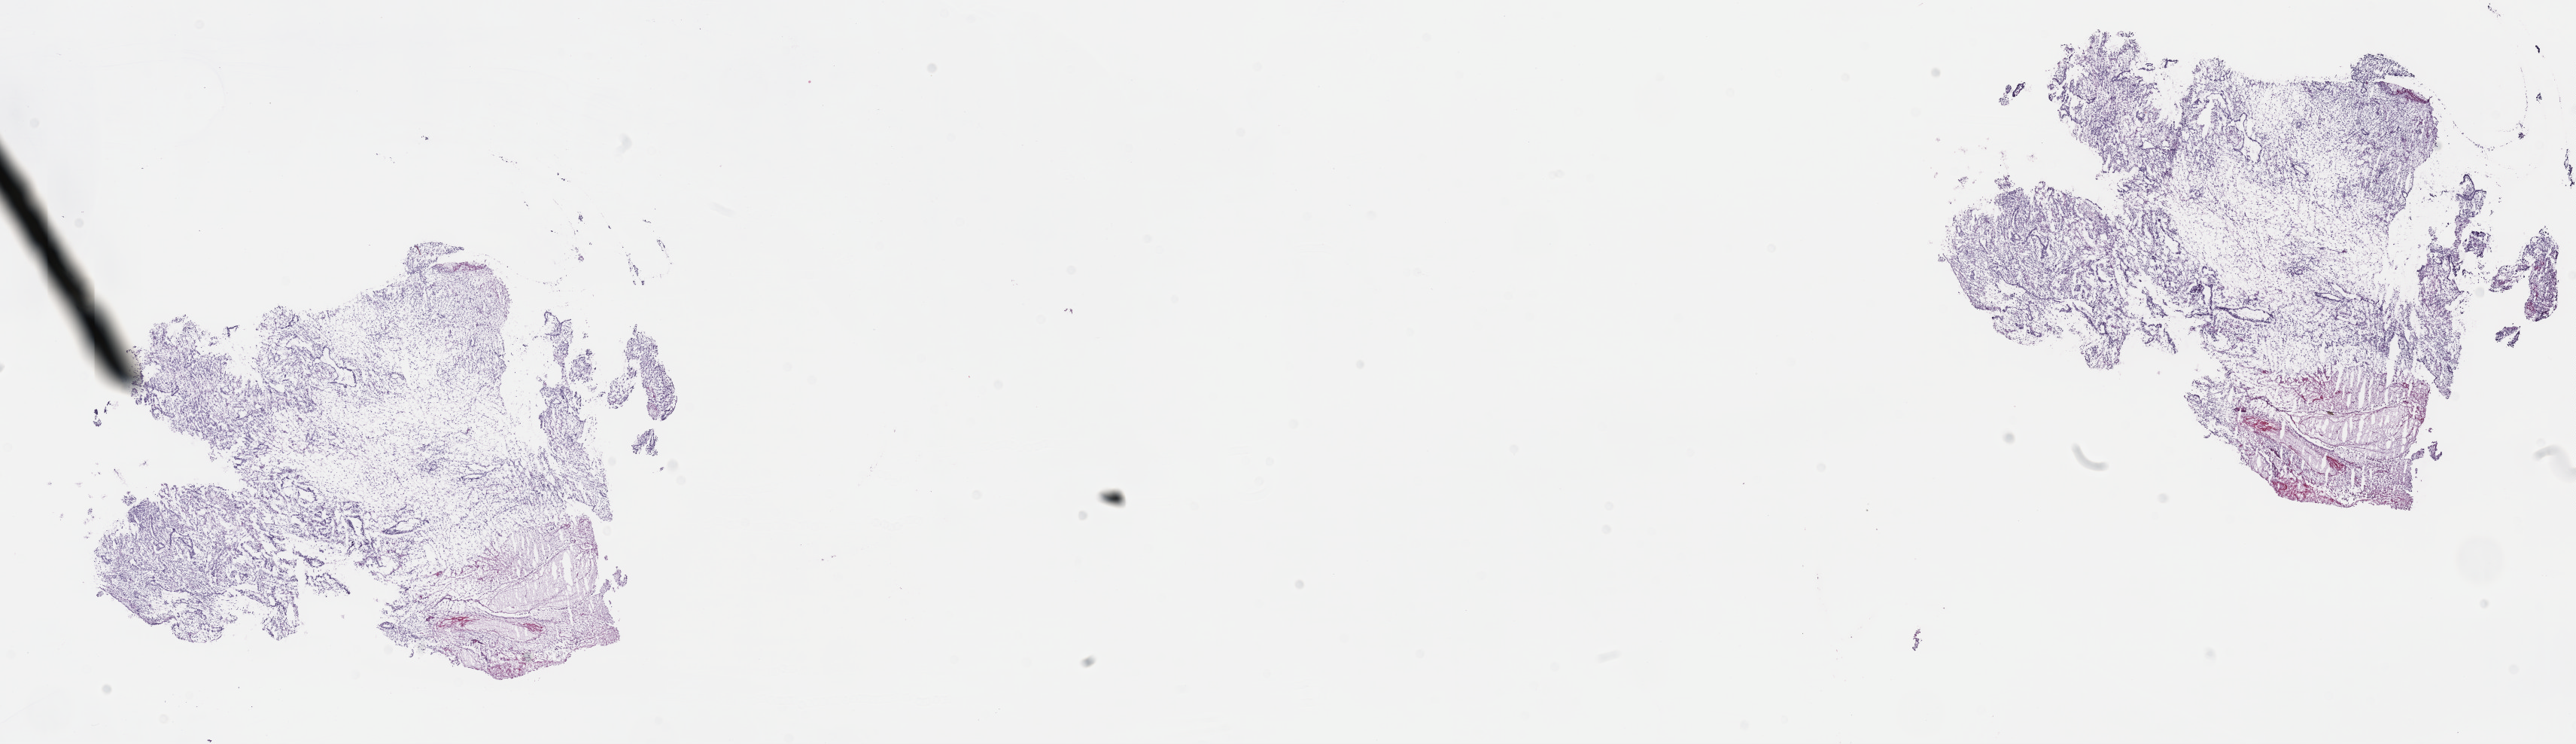
Digitized H&E tissue section (whole slide) — low-resolution overview of the scanned area, about 27.7 x 8.0 mm (slide scanned at 40x), frozen section from the top of the tissue portion, sample: primary tumour, testis. Male patient; age at initial diagnosis 31 years. Pathologist review of this section (percent, as recorded): tumour cells 90%, tumour nuclei 95%, normal cells 0%, stromal cells 10%, necrosis 0%. Inflammatory infiltration, as recorded: lymphocyte infiltration 0%, monocyte infiltration 0%, neutrophil infiltration 0%.
Histologic diagnosis: Mixed germ cell tumor. AJCC pathologic stage: I (4th edition).